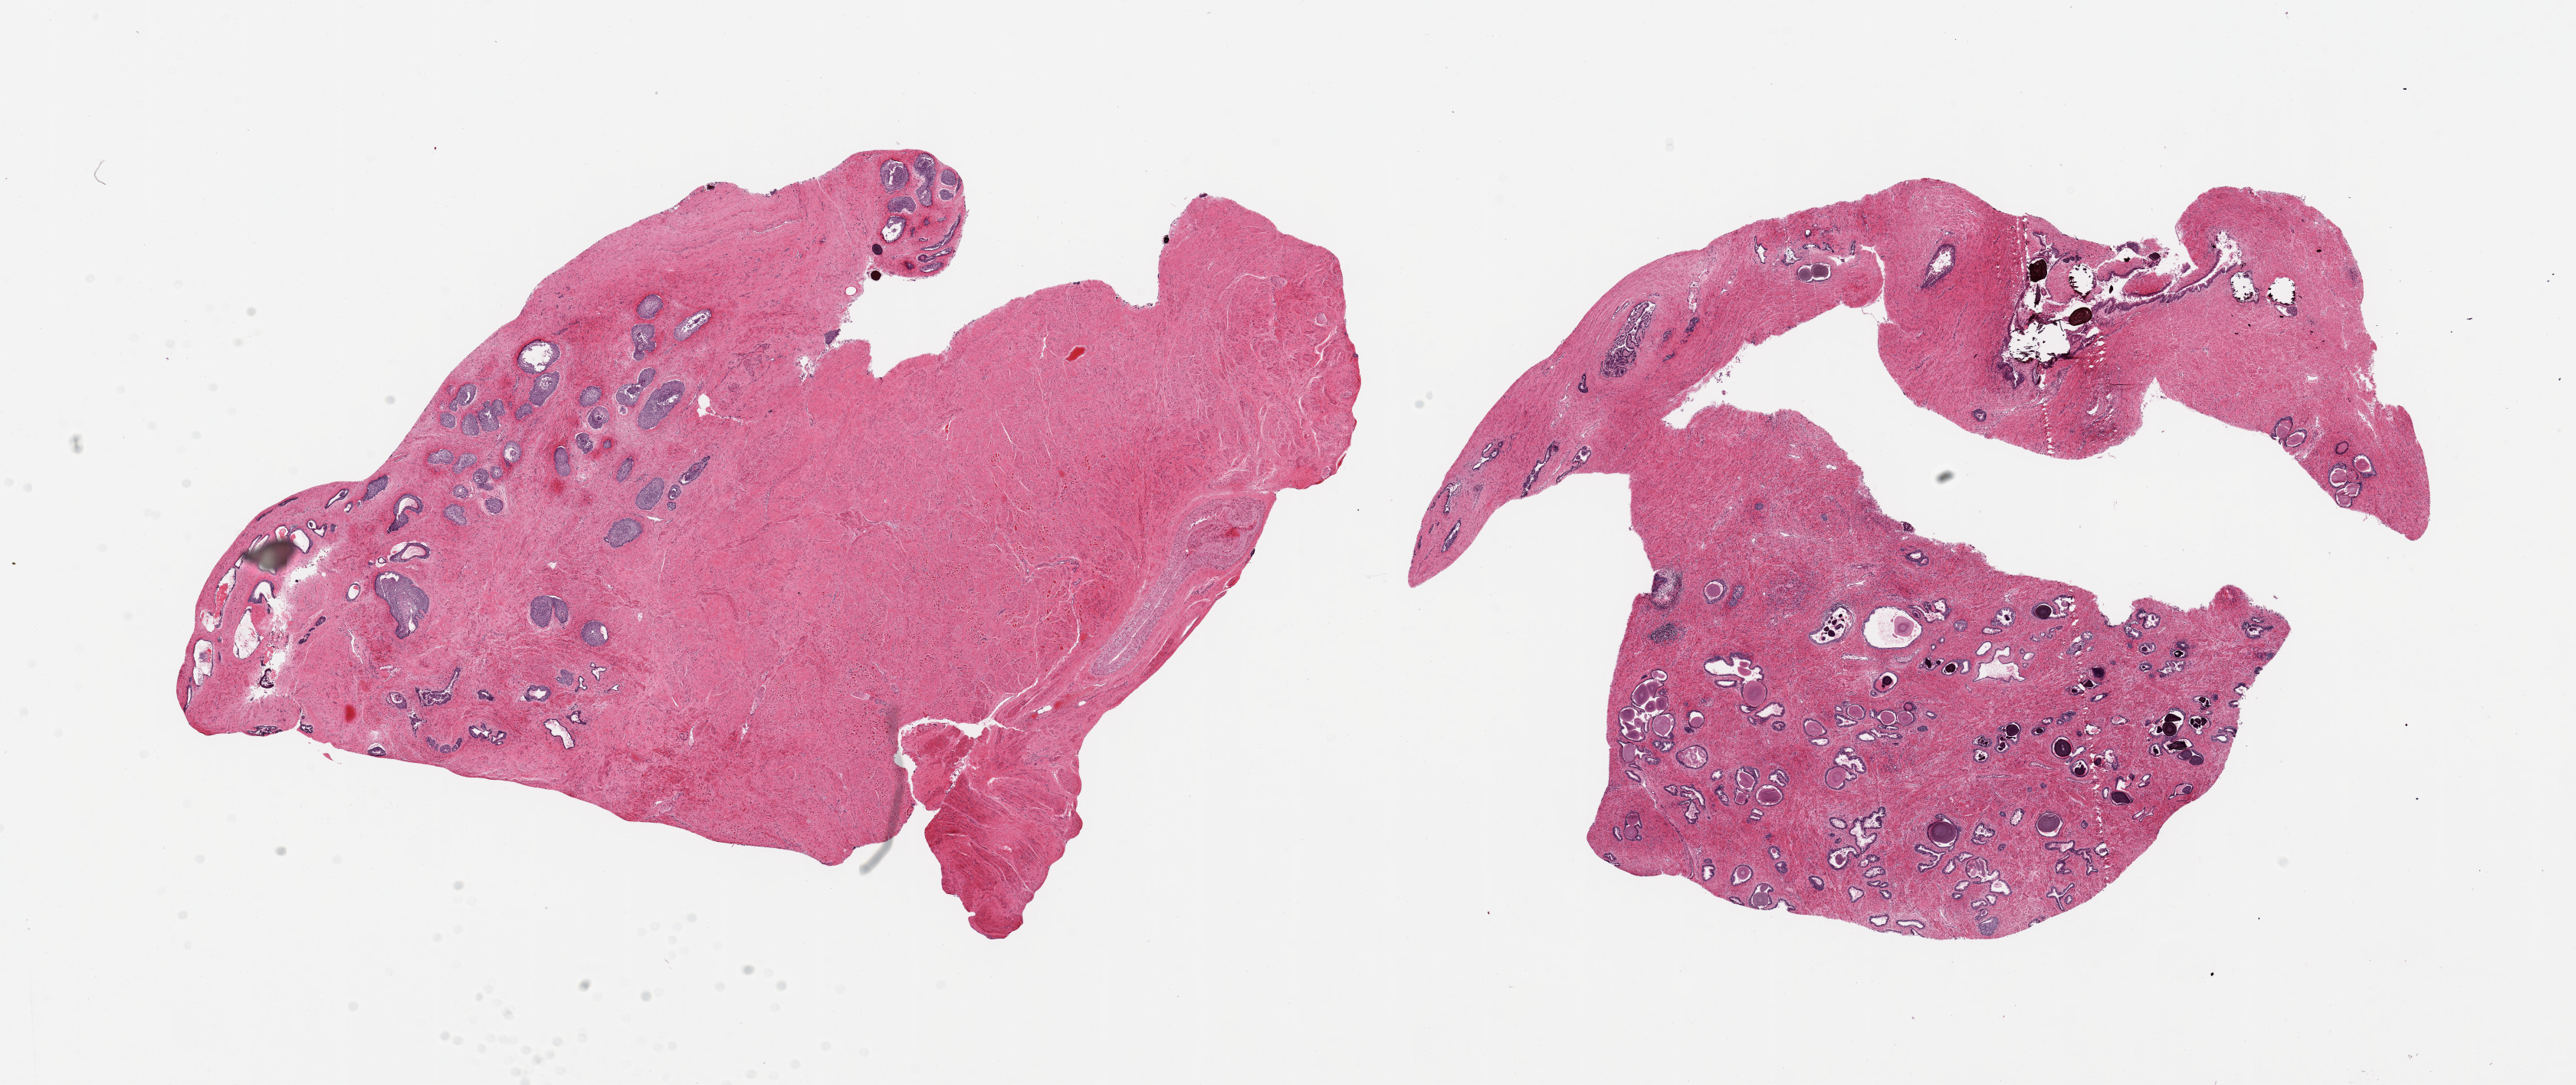
Whole-slide image, H&E stain — whole scanned area (about 26.6 x 11.2 mm, from a 20x scan) shown as a low-resolution overview. PAXgene-fixed, paraffin-embedded tissue. Section of prostate (target tissue). Donor tissue sample. Male donor.
- pathologist's review note for this sample: 2 pieces, prominent intraglandular calcospherules; glands with urothelial metaplasia